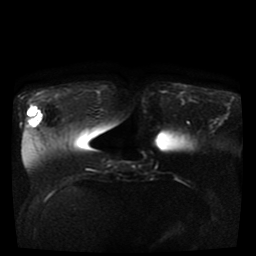
Breast MRI, one axial slice. Position 13 of 41 along the scan axis. Diffusion-weighted series; image 2 of 4 stored at this slice position (different b-values; order by instance number). 1.5 T. 5 mm slice thickness. 256 × 256 image matrix. Female patient.
Structures marked on this image (manually delineated by an expert):
- tumour on diffusion-weighted imaging: box from (x=29, y=110) to (x=42, y=126) px